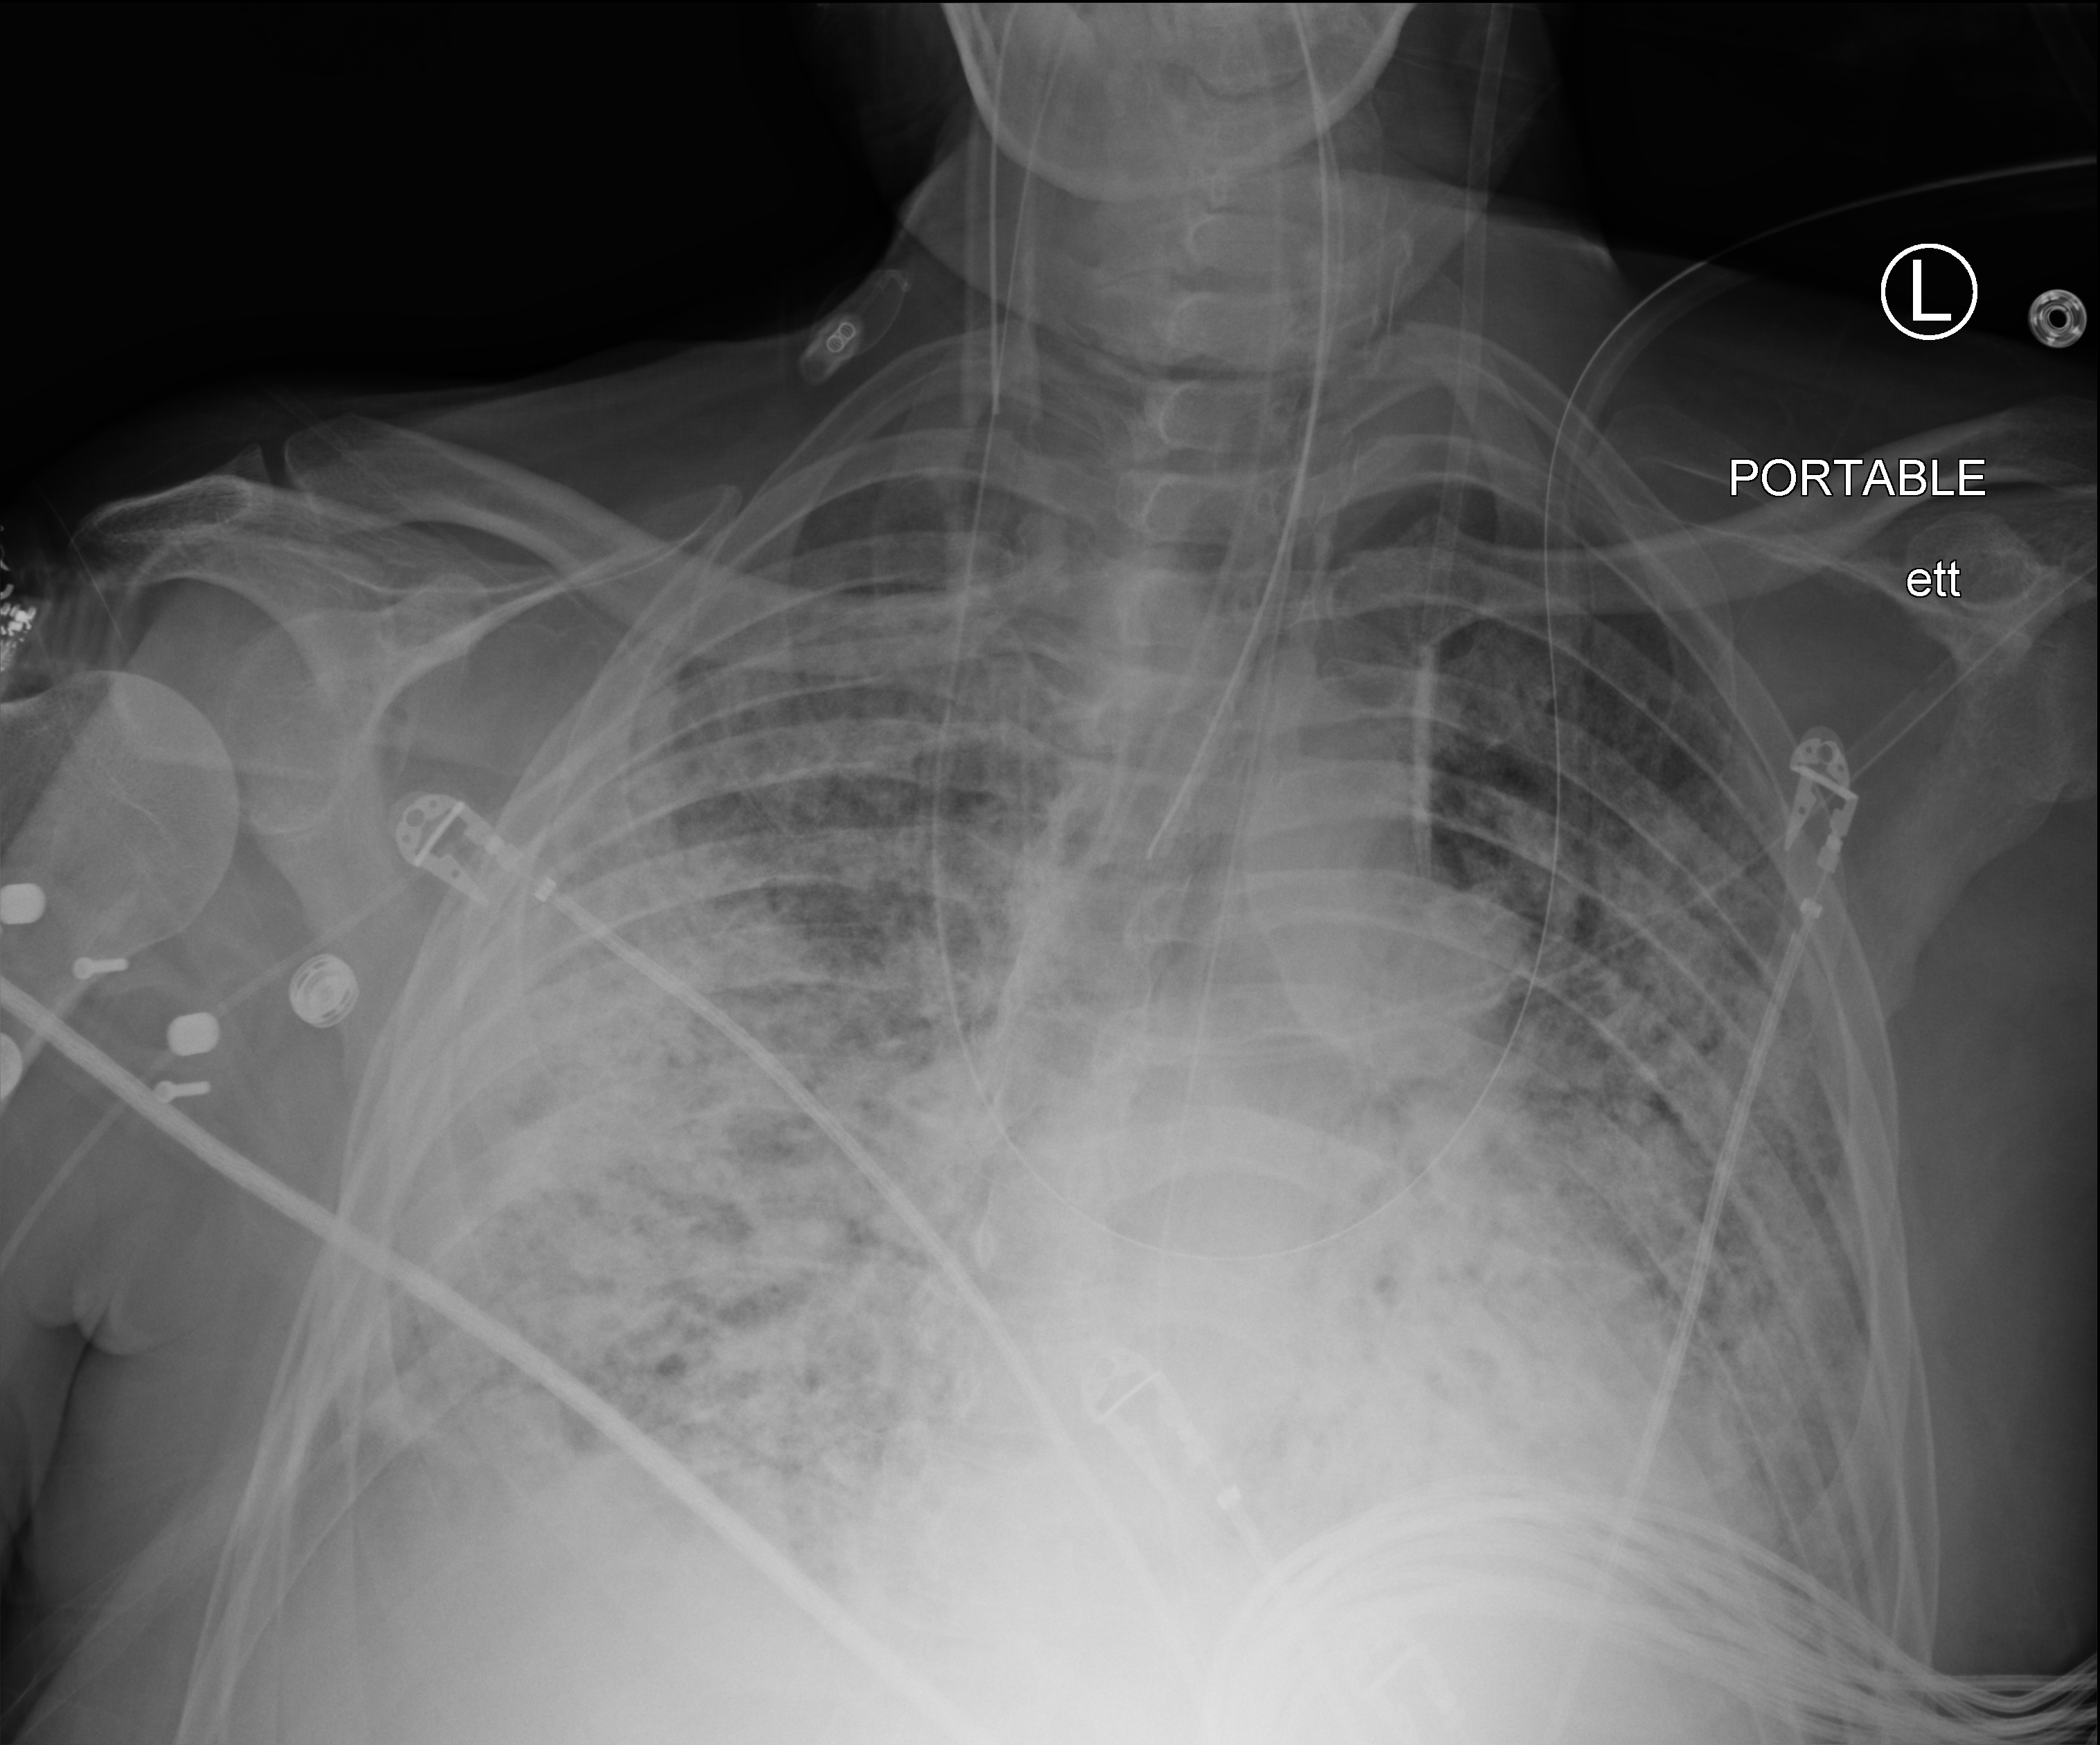
Chest X-ray (portable), anteroposterior (AP) projection. Male patient hospitalised with COVID-19, age 18–59 years.
Admission-level facts for this patient (not findings on this image; timing relative to this image not recorded):
- length of hospital stay: 75 days